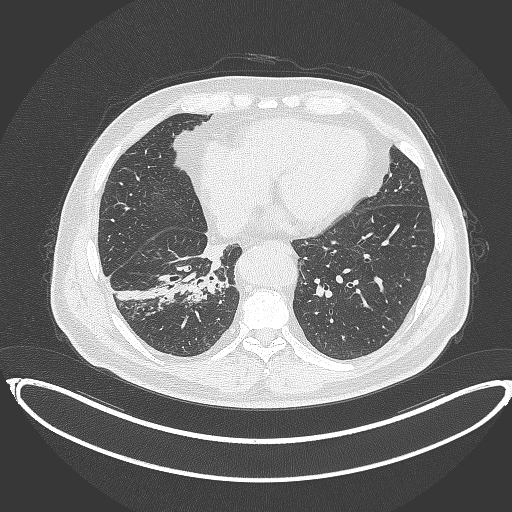
Chest CT, one axial slice. Position 140 of 387 along the scan axis. Reconstruction kernel B70f. 120 kVp. Lung window (W 1500 / L -600 HU). 1 mm slice thickness. 512 × 512 image matrix, field of view 448 × 448 mm. Male patient, age 61 years. Case-level facts recorded for this patient, not image findings: clinical TNM (as recorded): T1b N1 M0.
Structures marked on this image (bounding box drawn by a radiologist):
- lung tumour (recorded histology: squamous cell carcinoma): bounding box [x1, y1, x2, y2] px = [179, 268, 227, 307]